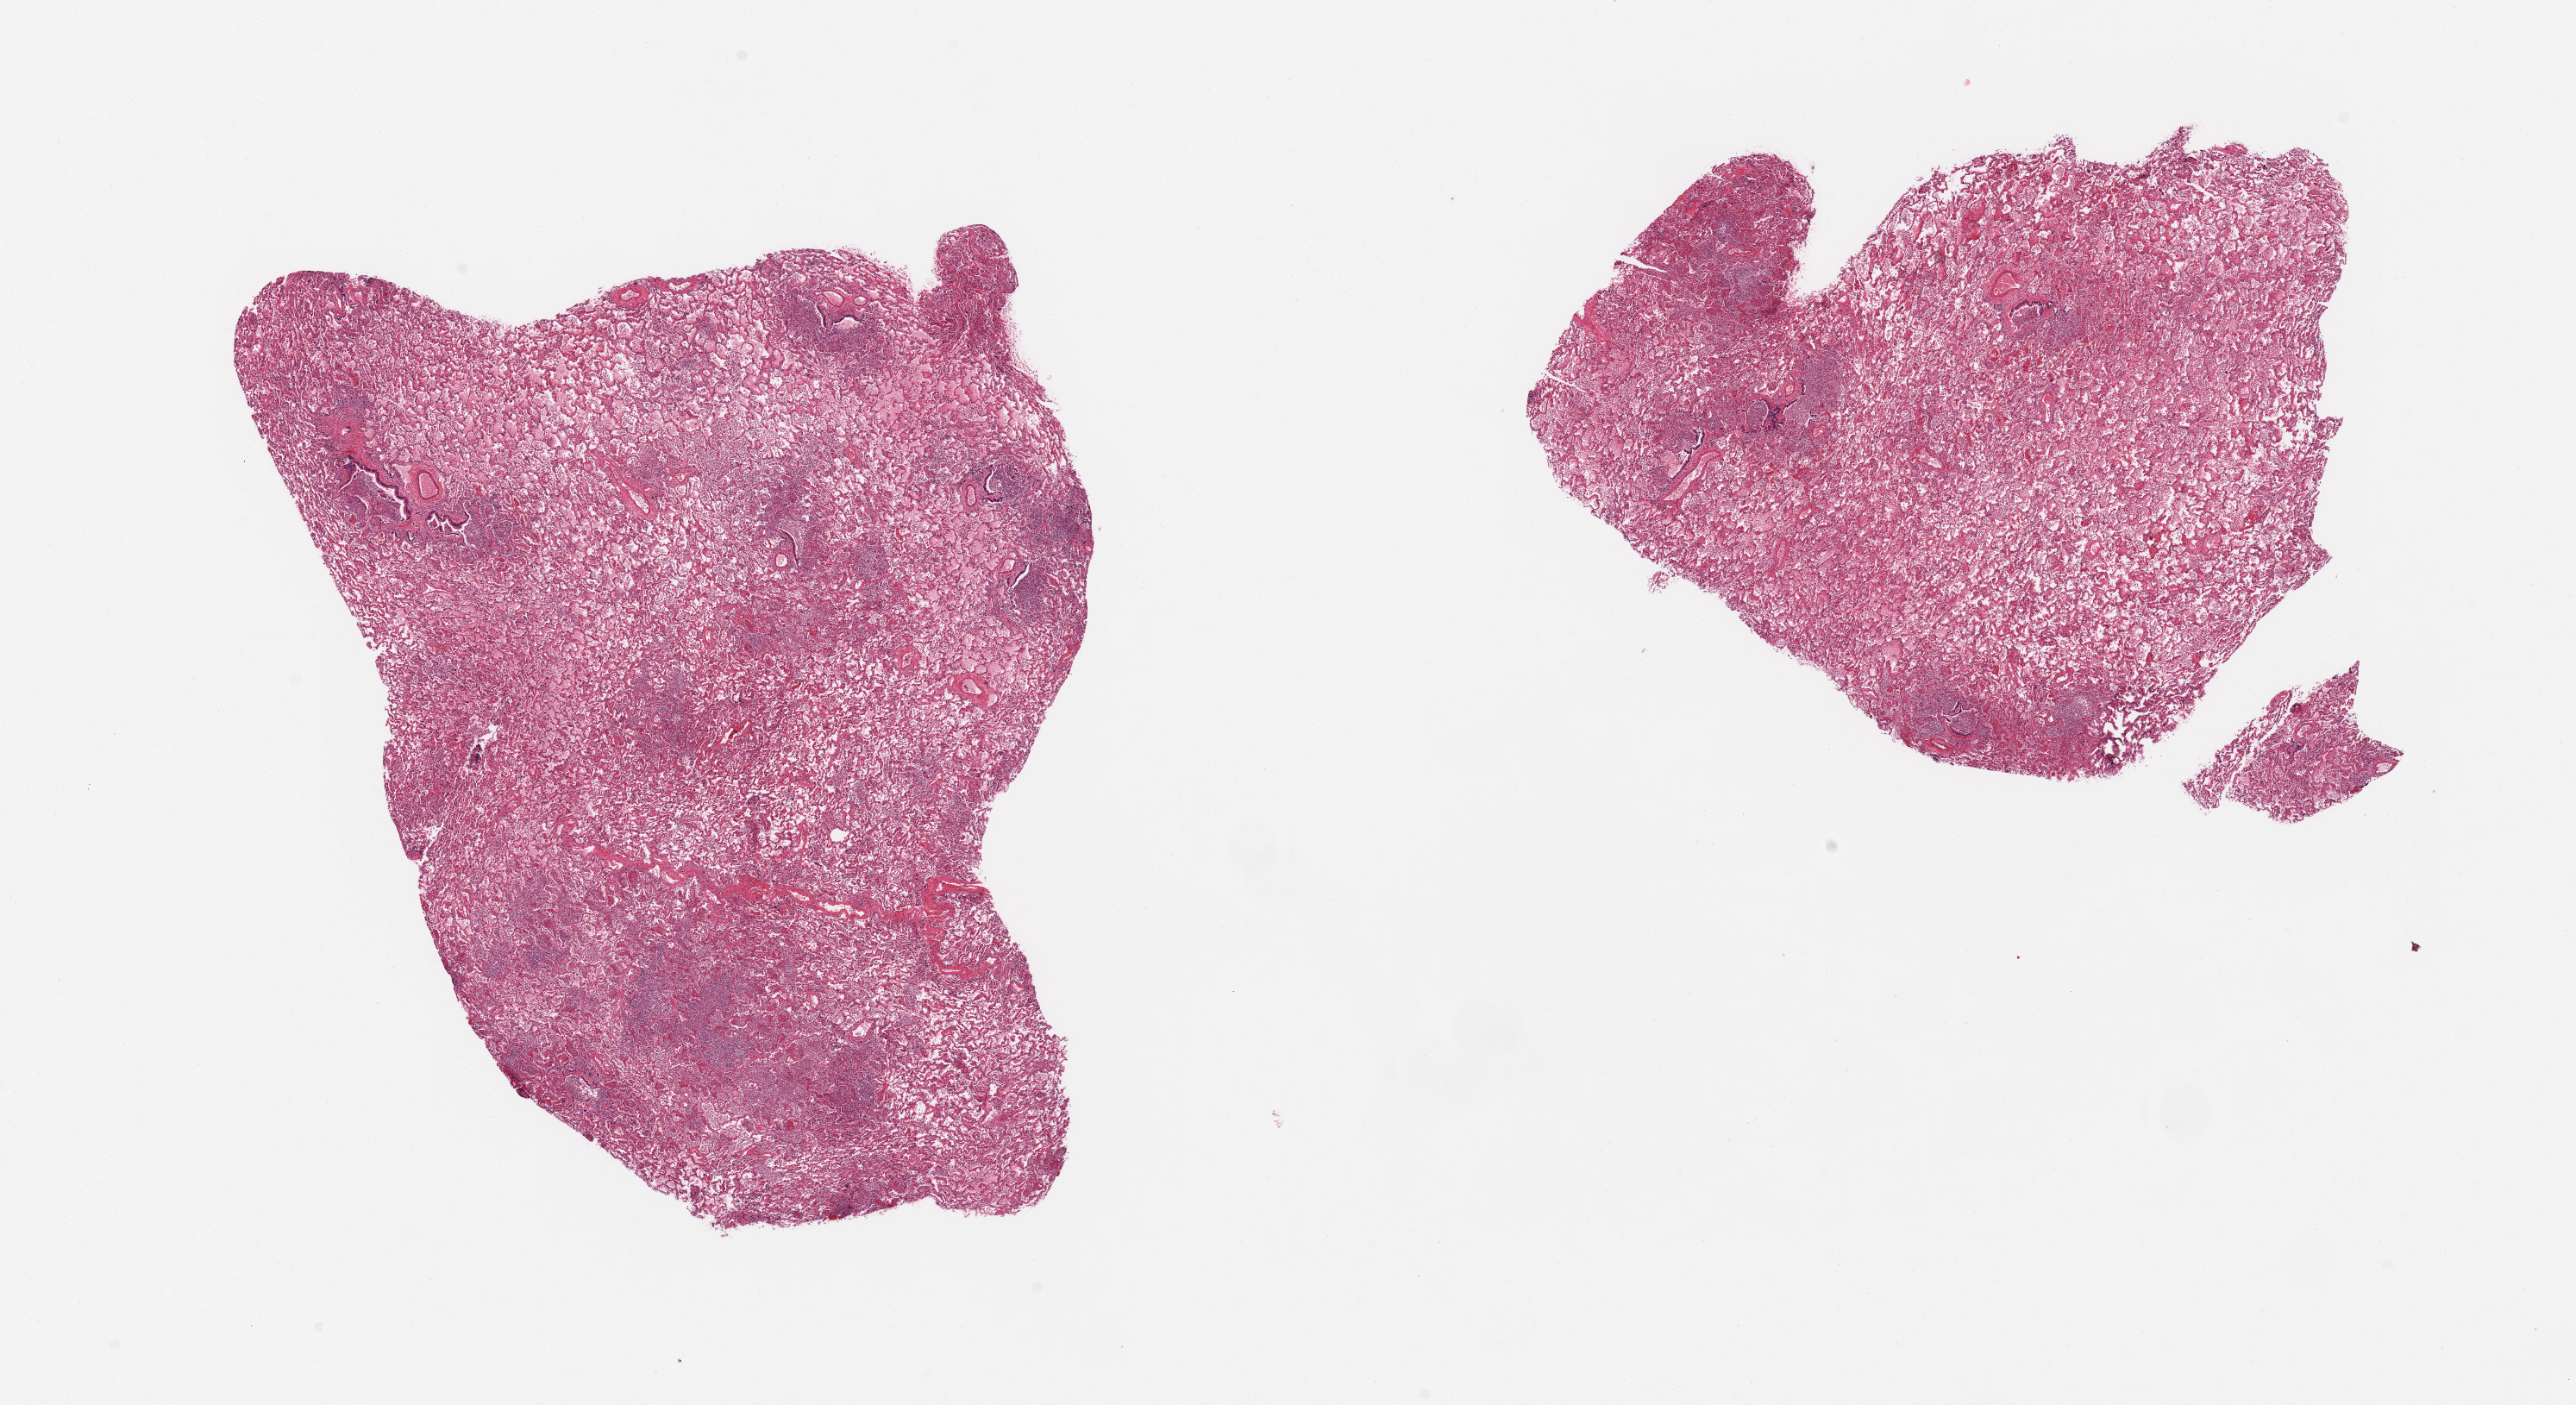
Whole-slide image, haematoxylin and eosin stain, whole scanned area (about 23.6 x 12.9 mm, acquisition: 20x scan) shown as a low-resolution overview, PAXgene-fixed, paraffin-embedded tissue, section of lung (target tissue), donor tissue sample. Donor sex: male.
Pathologist's review note for this sample: 2 pieces, diffuse acute pneumonia, focally necrotizing.